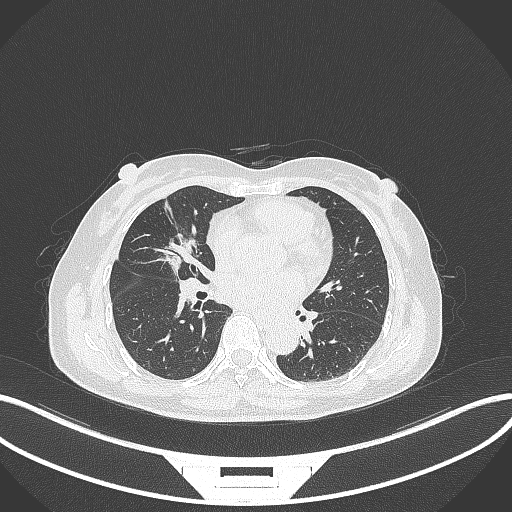
Chest CT, one axial slice. Slice 143 of 284 in the series (ordered by position). Reconstruction kernel B70f. 120 kVp. Lung window (W 1500 / L -600 HU). 512 × 512 image matrix, field of view 400 × 400 mm. Patient: female, 51 years. Case-level facts recorded for this patient, not image findings: clinical TNM (as recorded): T1c N0 M0; histopathological grade: G2.
Structures marked on this image (bounding box drawn by a radiologist):
- lung tumour (recorded histology: adenocarcinoma): bounding box <162,232,200,272> (left, top, right, bottom; pixels)